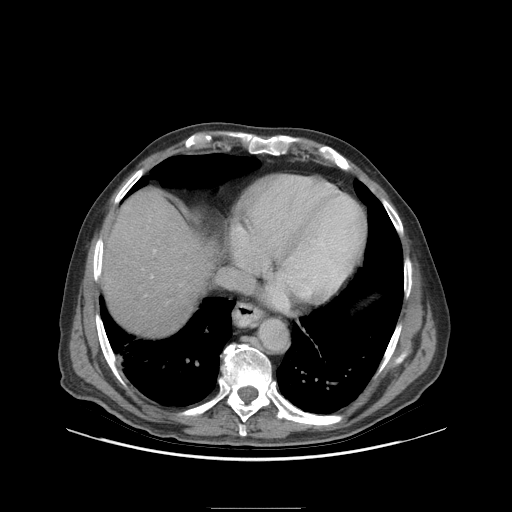
Contrast-enhanced abdominal CT (liver protocol), one axial slice; slice 88 of 105 in the series (ordered by position); soft-tissue window (W 400 / L 40 HU); 2.5 mm slice thickness; 512 × 512 image matrix, field of view 440 × 440 mm. Case-level facts recorded for this patient, not image findings: diagnosis: hepatocellular carcinoma (patient treated with transarterial chemoembolisation; whether this scan precedes or follows treatment is not stated here); TNM stage (as recorded): Stage-I; Child-Pugh class: A.
Annotated regions visible in this slice (semi-automatic segmentation, software-assisted and operator-edited):
- liver parenchyma outside the tumour (the mass and vessels are separate outlines, so this box may not span the whole liver): bounding box <100,188,208,336> (left, top, right, bottom; pixels)
- liver vessels: <154,249,156,252>